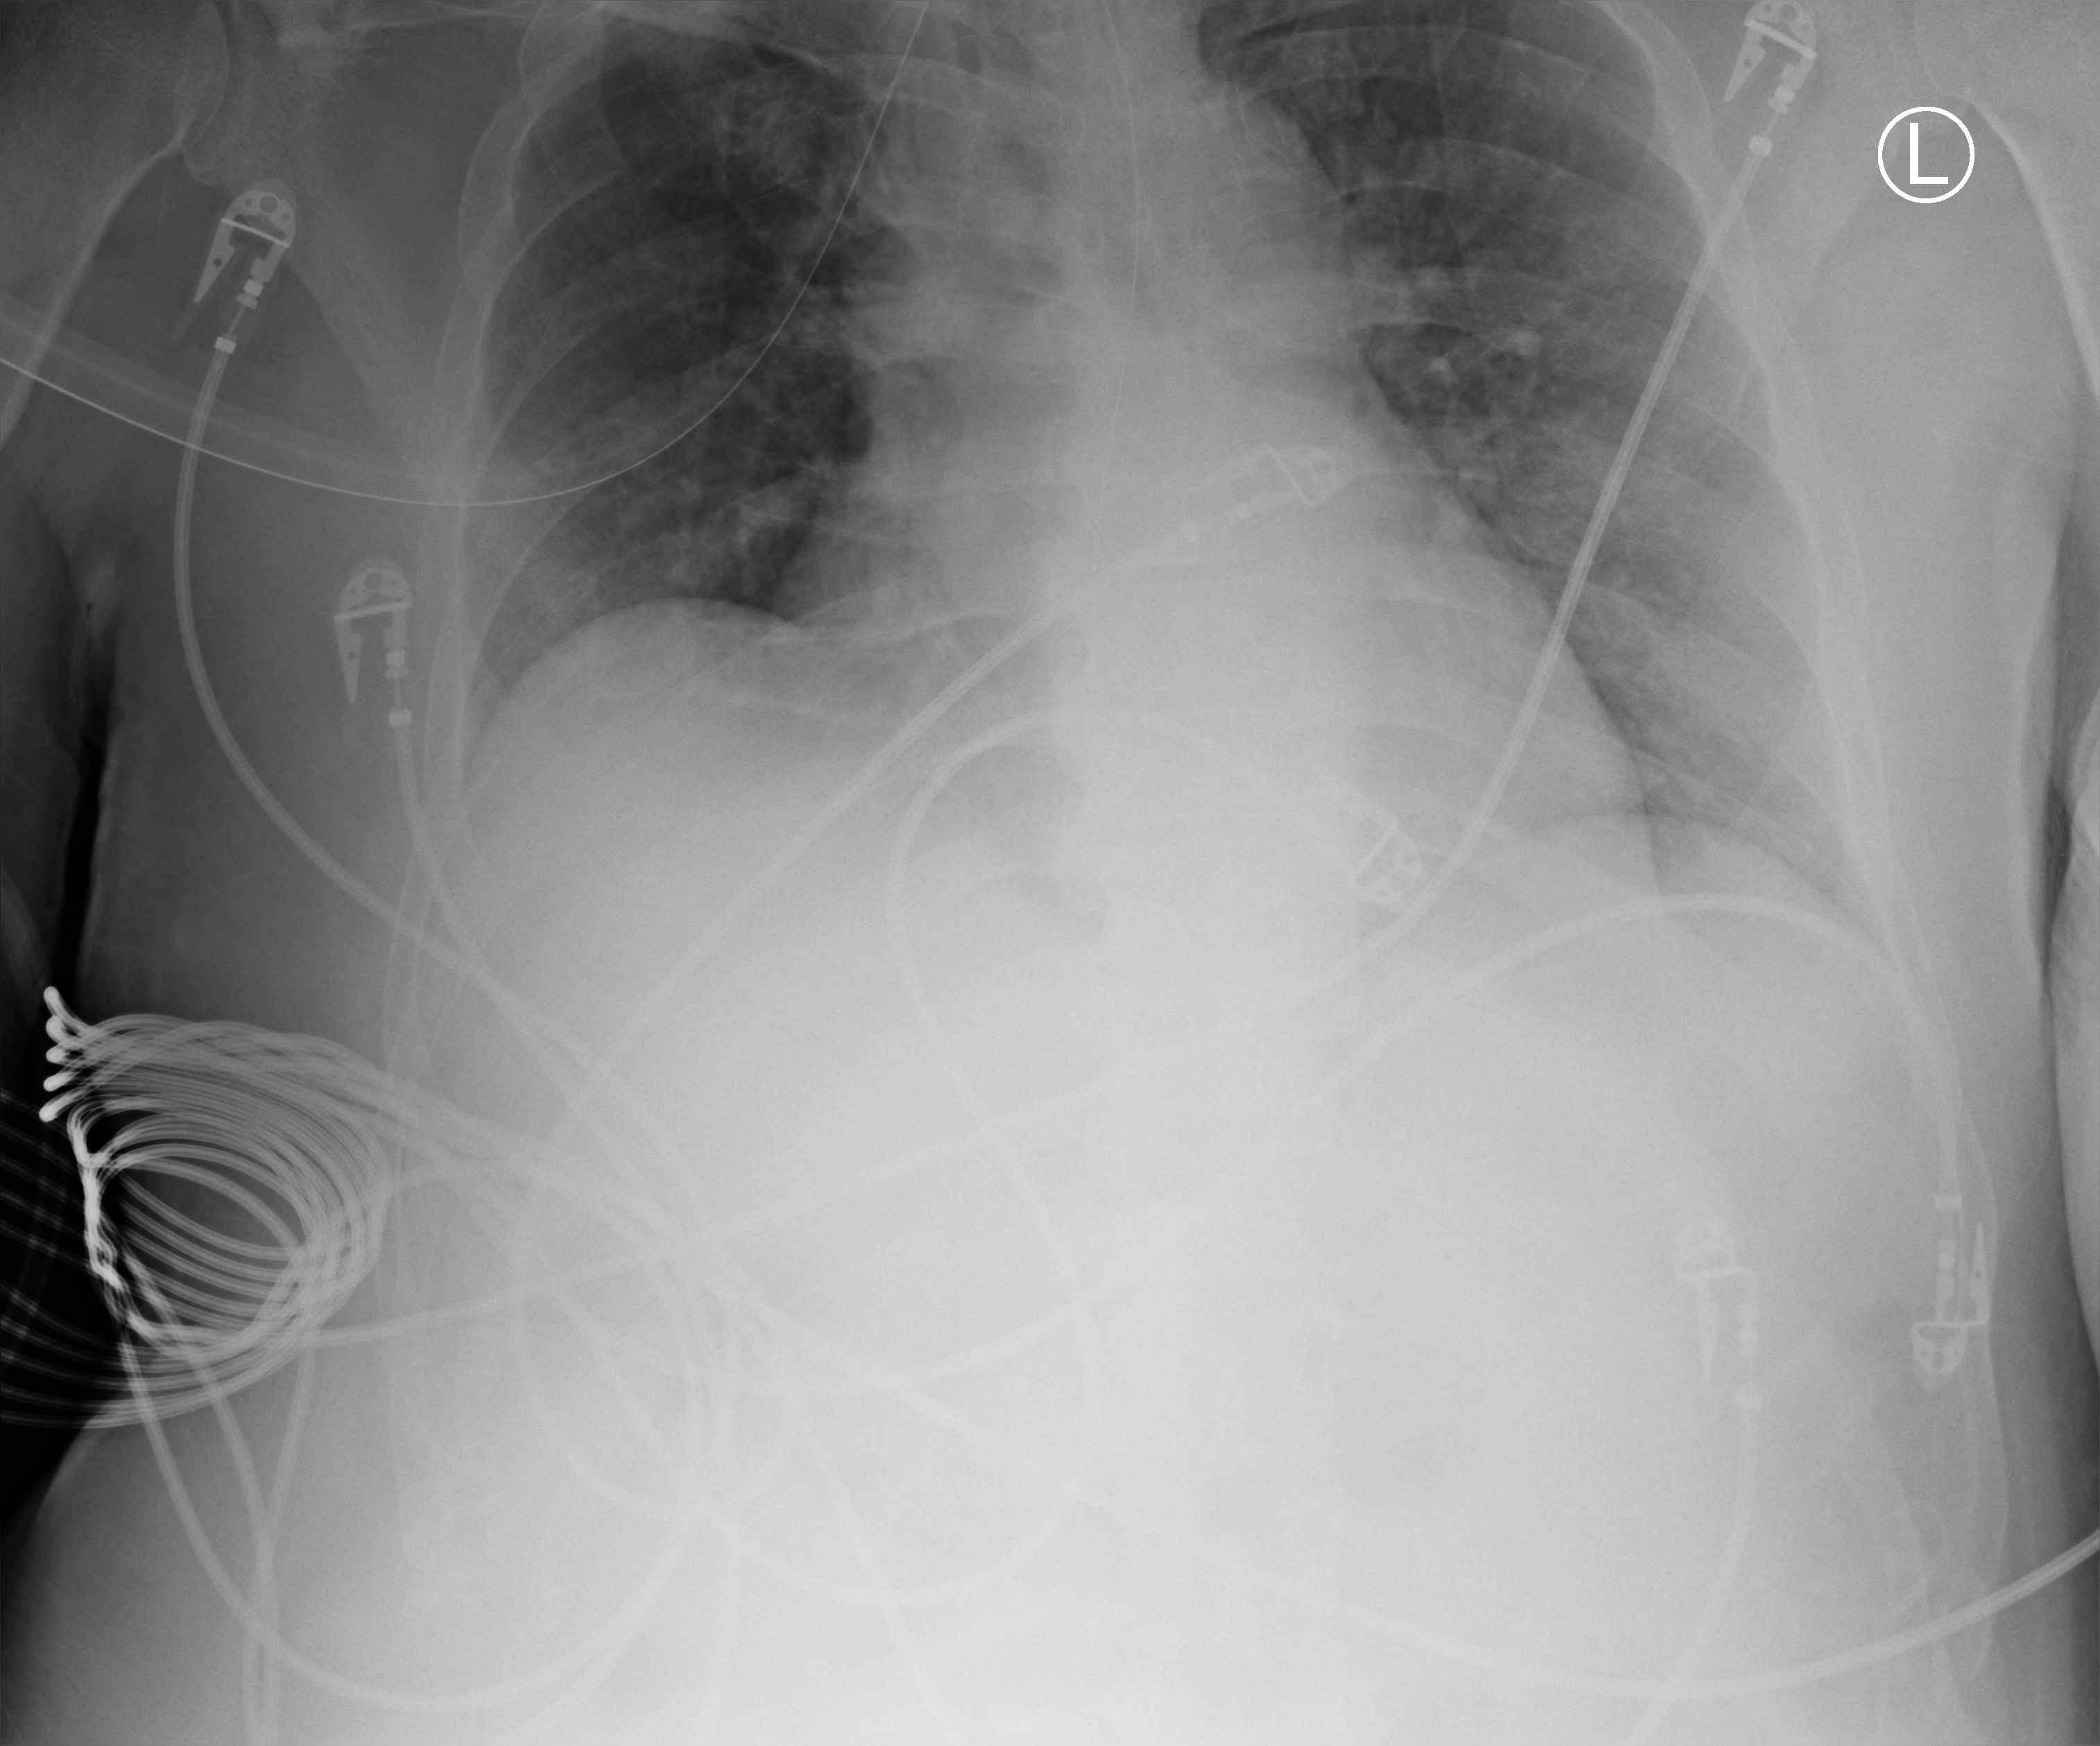
Bedside chest radiograph (computed radiography). Adult patient hospitalised with COVID-19, age 18–59 years.
Admission-level facts for this patient (not findings on this image; timing relative to this image not recorded):
- mechanically ventilated during this hospital stay: yes
- admitted to intensive care during this hospital stay: yes